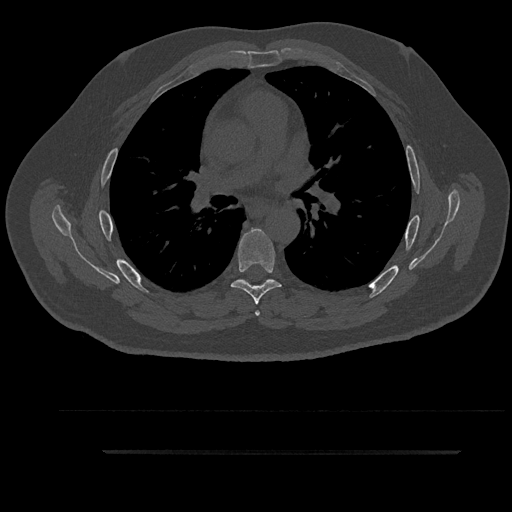
CT including the spine, one axial slice; position 579 of 797 along the scan axis; 120 kVp; bone window (W 1800 / L 400 HU); 0.5 mm slice thickness; 512 × 512 image matrix, field of view 432 × 432 mm. Patient: male, 63 years. Case-level facts recorded for this patient, not image findings: primary cancer: renal; vertebrae with lytic lesions (as recorded): T8.
Annotated regions visible in this slice (semi-automatic segmentation, software-assisted and operator-edited):
- T5 vertebra: box from (x=238, y=279) to (x=271, y=316) px
- T6 vertebra: (x=231, y=229)–(x=281, y=305)